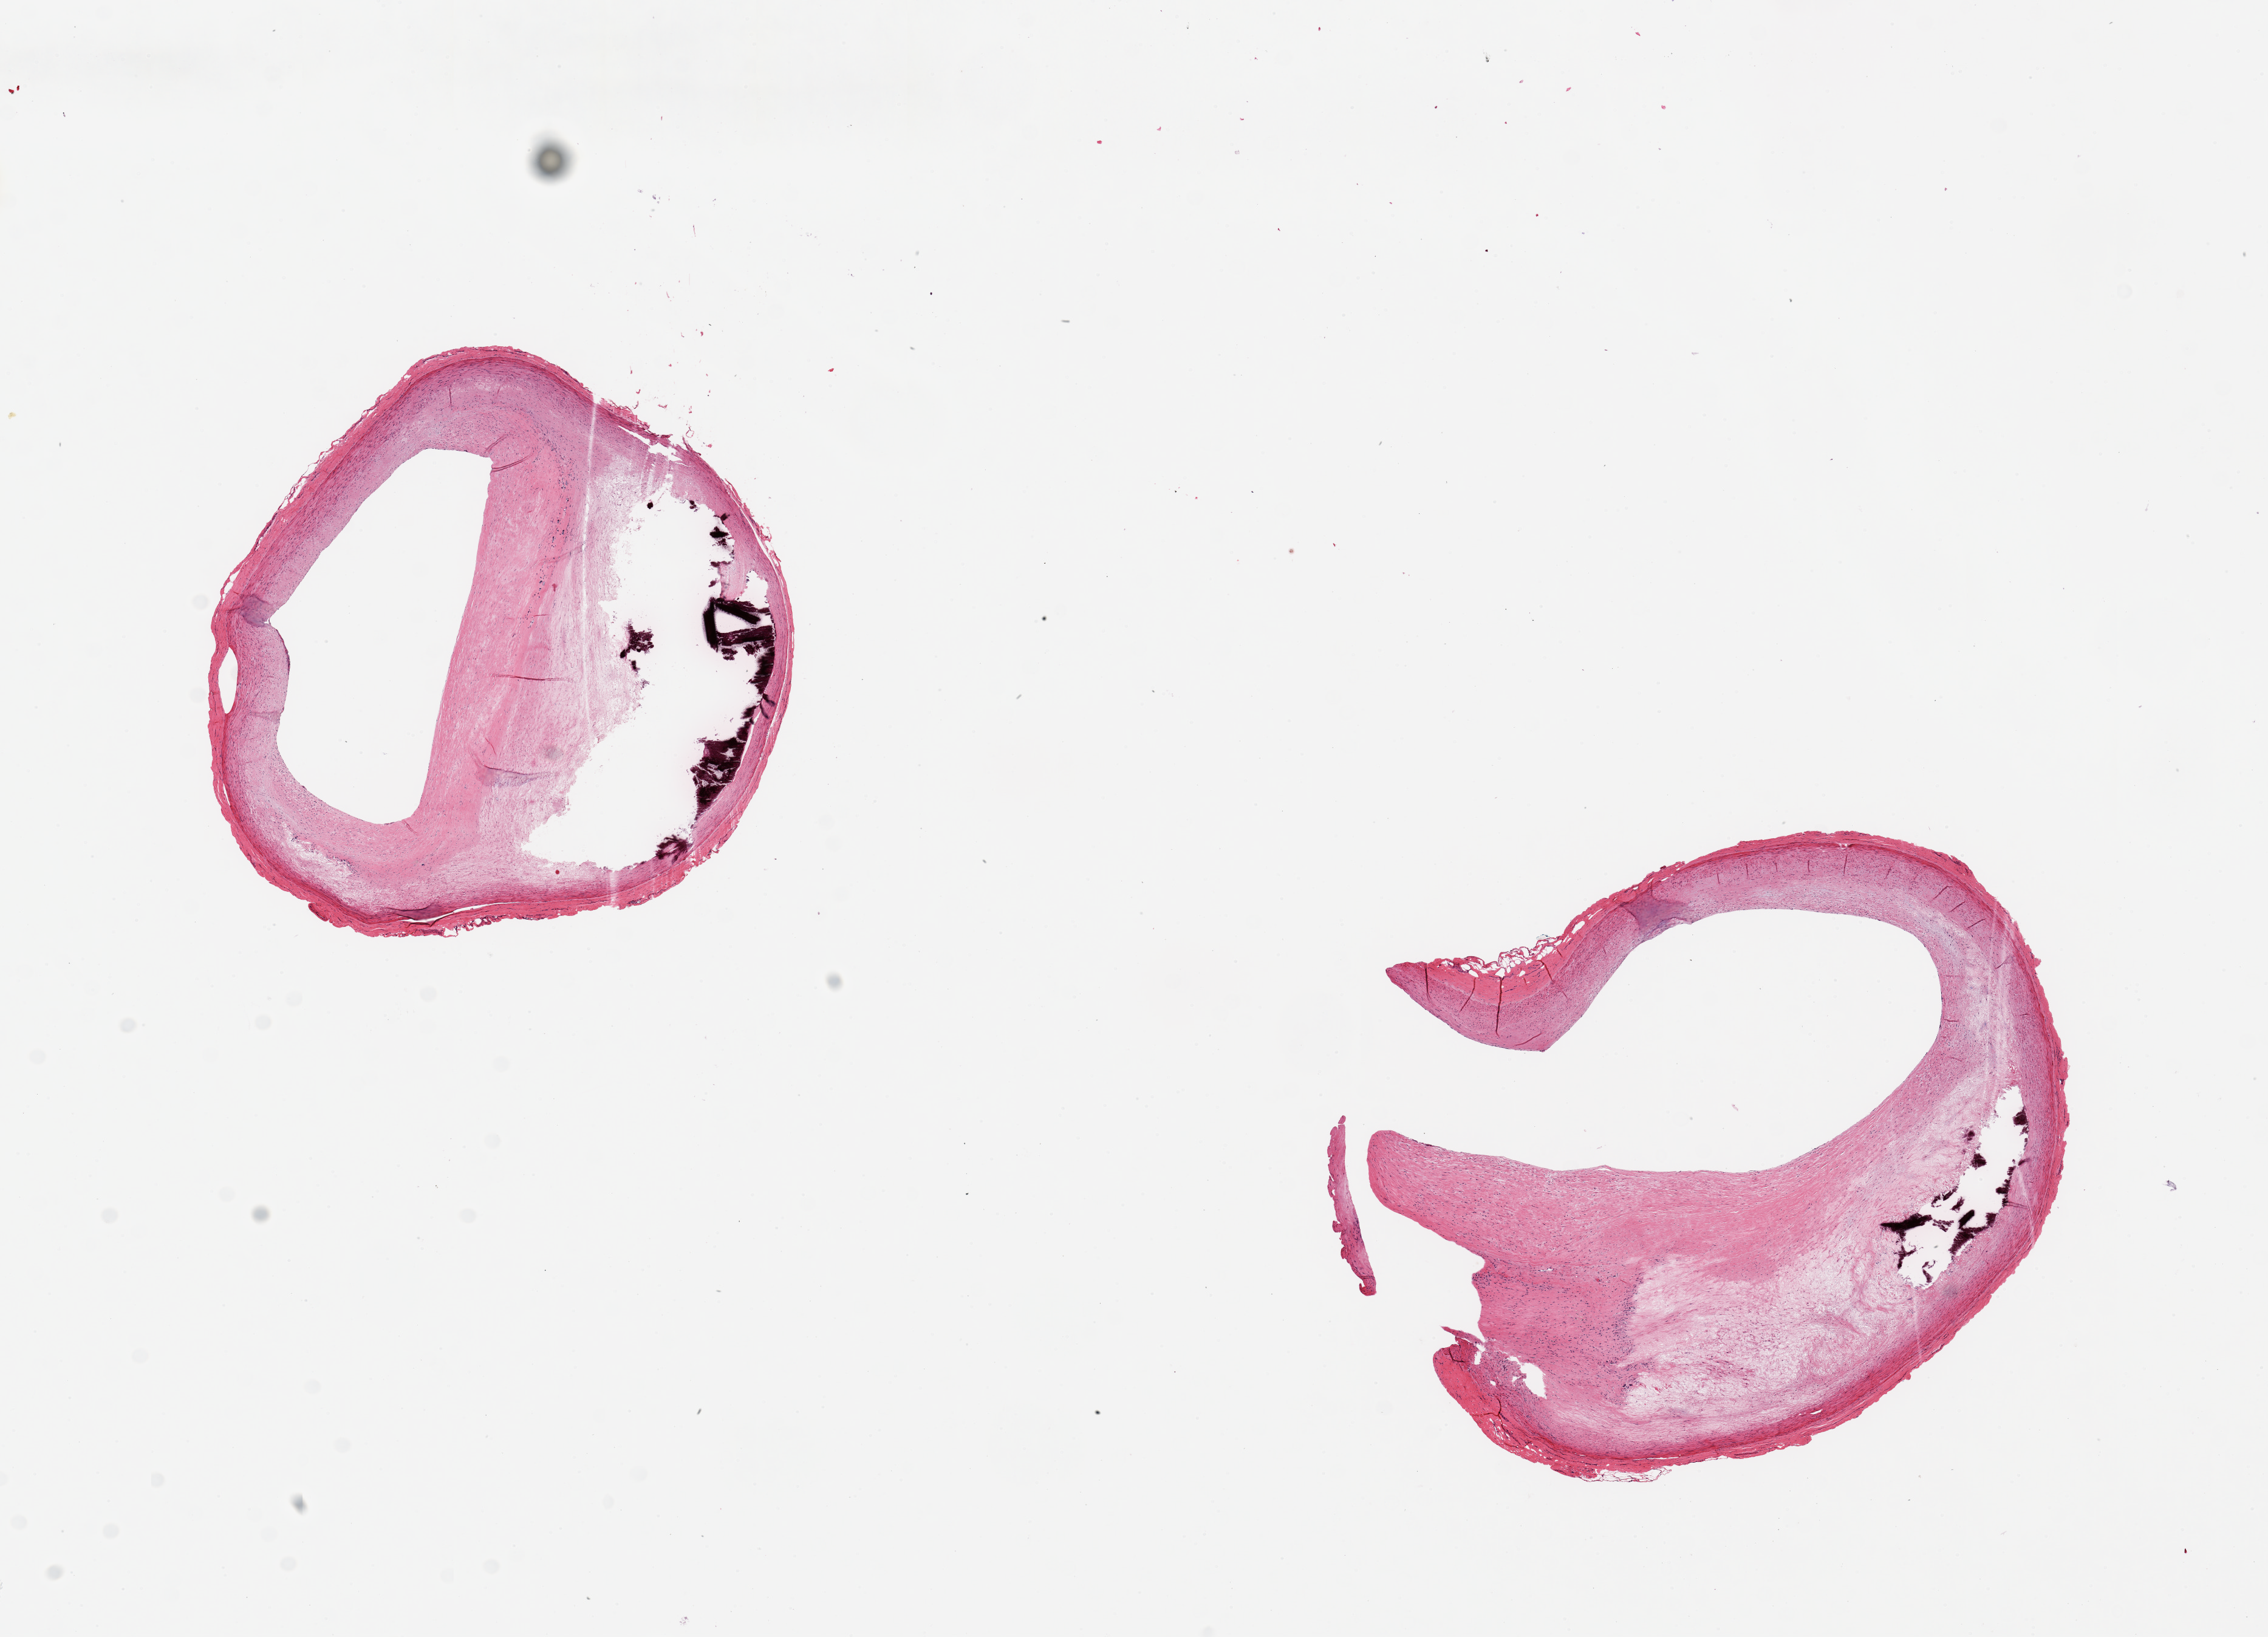
Whole-slide image, haematoxylin and eosin stain, low-resolution overview of the scanned area, about 14.8 x 10.7 mm; PAXgene-fixed, paraffin-embedded tissue; target tissue: coronary artery; tissue donor sample. Donor sex: male.
Reviewer comment on this tissue sample: 2 pieces ~3.5mm d; 50% occlusive, calcifying atherosclerosis.